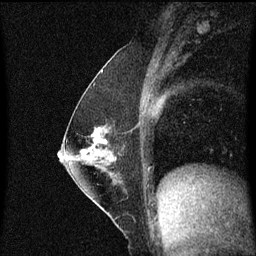
Breast MRI (dynamic contrast-enhanced), one sagittal slice; position 29 of 60 along the scan axis; dynamic contrast-enhanced series, image 2 of 3 at this slice position (ordered by acquisition); 1.5 T; TE 4.2 ms, TR 8.4 ms; 2 mm slice thickness; 256 × 256 image matrix. Female patient, age 52 years. Case-level facts recorded for this patient, not image findings: setting: breast cancer imaged before/during neoadjuvant chemotherapy; receptor status: HER2-positive.
Annotated regions visible in this slice (semi-automatically segmented with operator editing):
- analysis volume of interest (the breast-tissue region the enhancement analysis was run in; not a lesion): bounding box (x1, y1, x2, y2) in pixels: (71, 118, 126, 187)
- tumour enhancement mask (voxels above the 70 % enhancement threshold inside the analysis volume of interest): (93, 132, 107, 143)